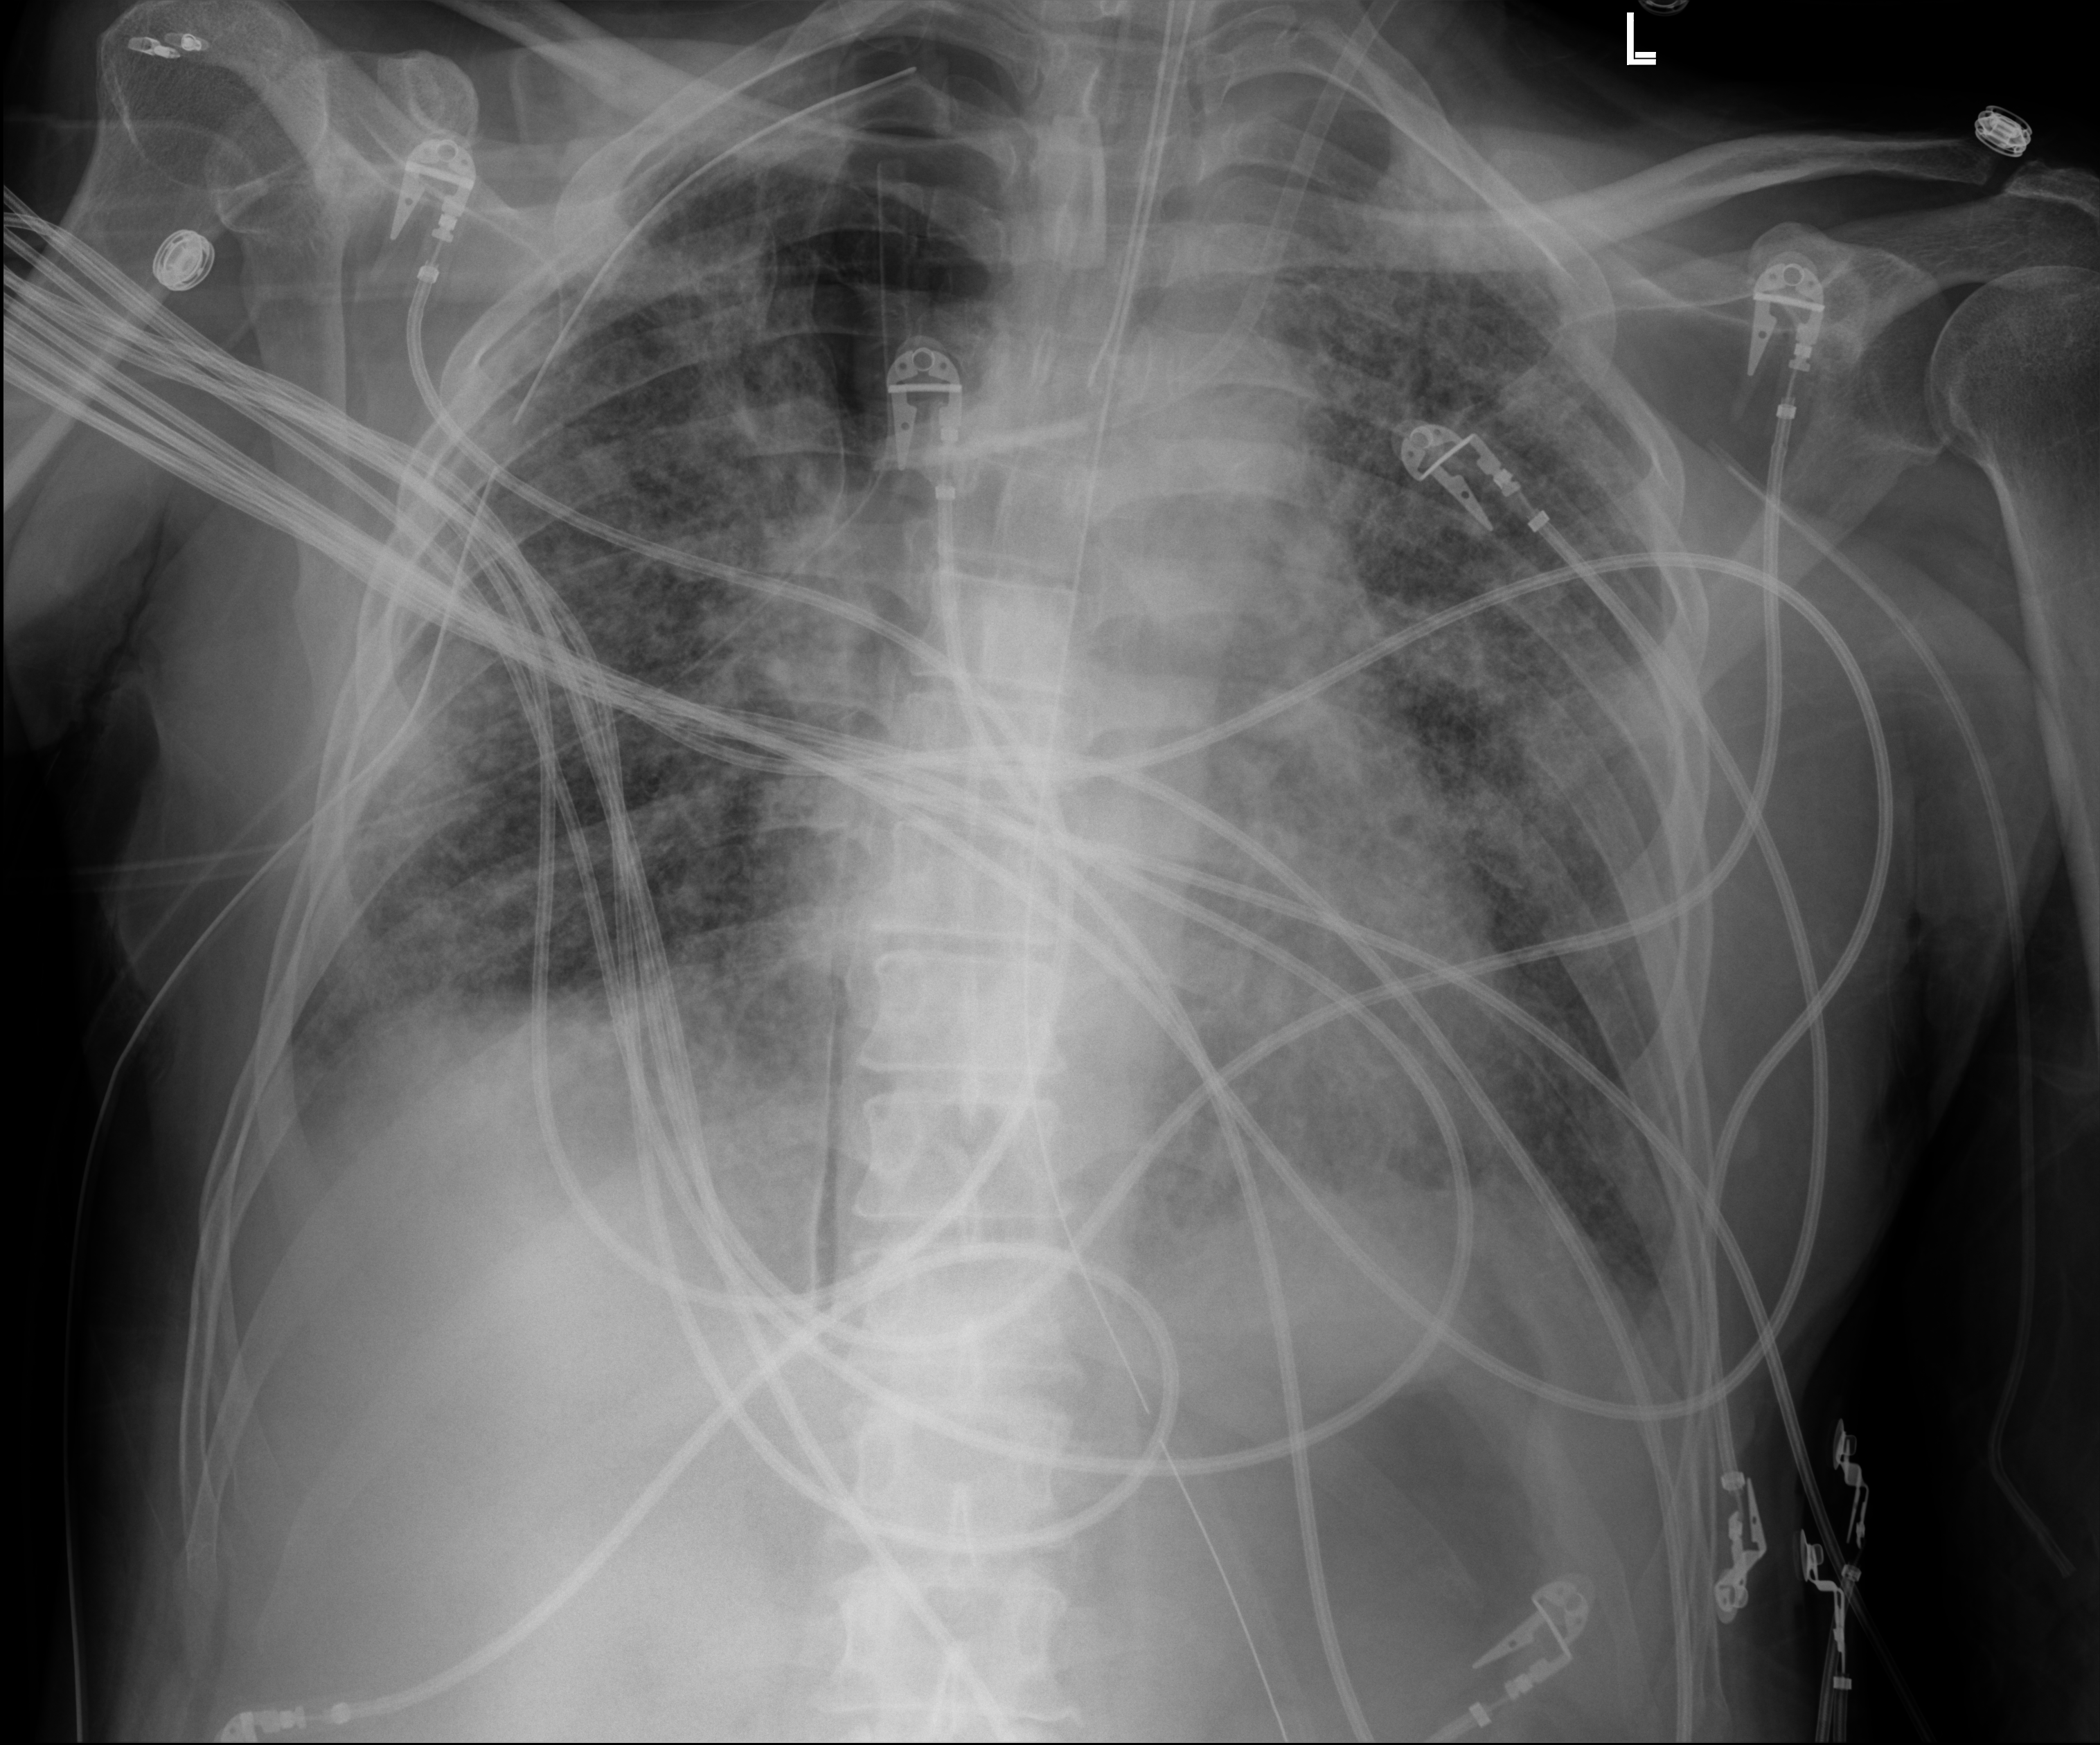
Portable chest radiograph, anteroposterior (AP) projection. Patient hospitalised with COVID-19; male, aged 60–74 years.
From the hospital-stay record, not from the radiograph (when in the stay this image was taken is not recorded):
- length of hospital stay: 65 days
- mechanically ventilated during this hospital stay: yes
- admitted to intensive care during this hospital stay: yes